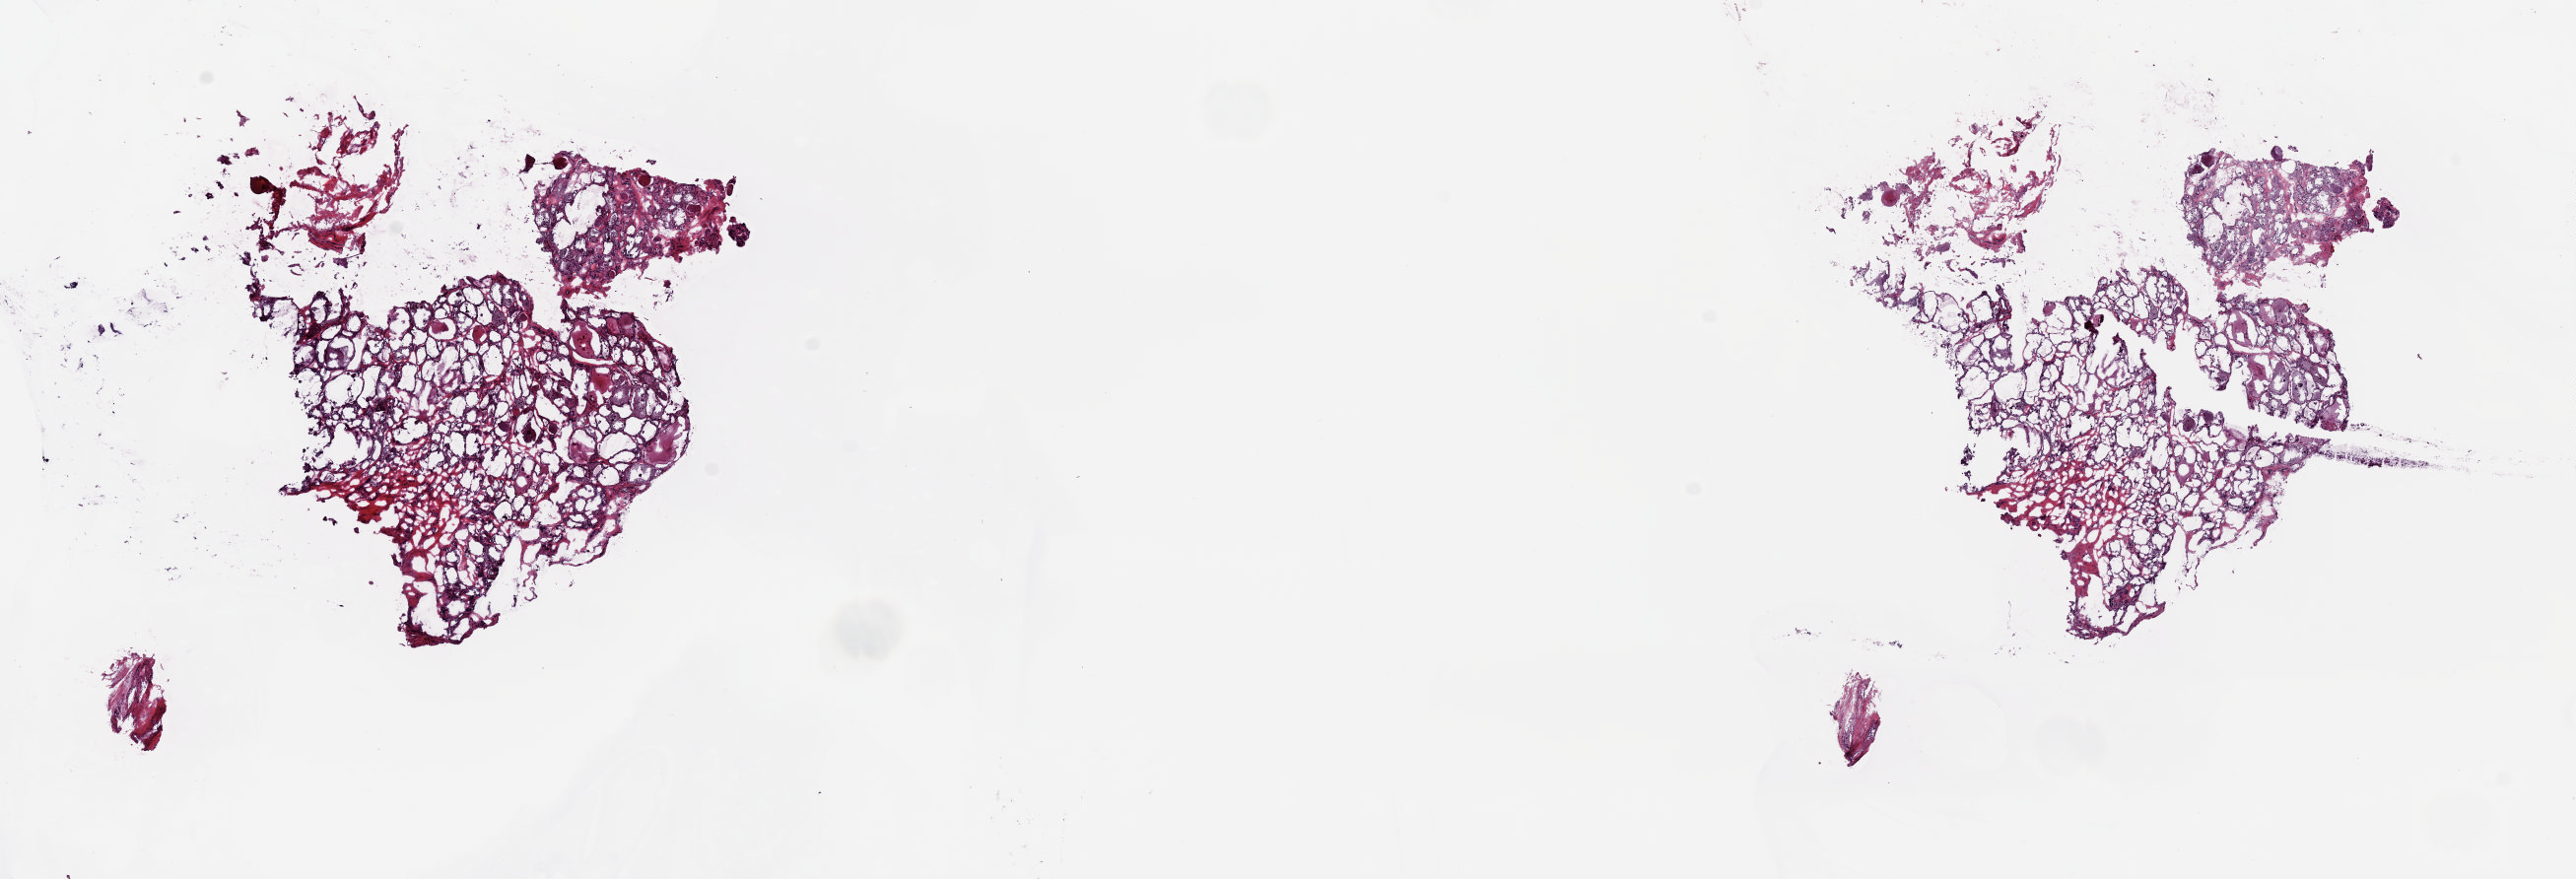
Whole-slide histology image, Hematoxylin and eosin (H&E) stained — low-resolution overview of the scanned area, about 20.7 x 7.1 mm (slide scanned at 20x); frozen section from the top of the tissue portion; solid tissue normal (non-tumour tissue) sample from the thyroid. Male patient; age at initial diagnosis 36 years. Pathologist review of this section (percent, as recorded): tumour cells 0%, tumour nuclei 0%, normal cells 100%, stromal cells 0%, necrosis 0%. Infiltration values recorded for this section: lymphocyte infiltration 0%, monocyte infiltration 0%, neutrophil infiltration 0%.
This section: solid tissue normal (non-tumour) sample from the same patient. Patient diagnosis: Papillary adenocarcinoma, NOS (thyroid gland).